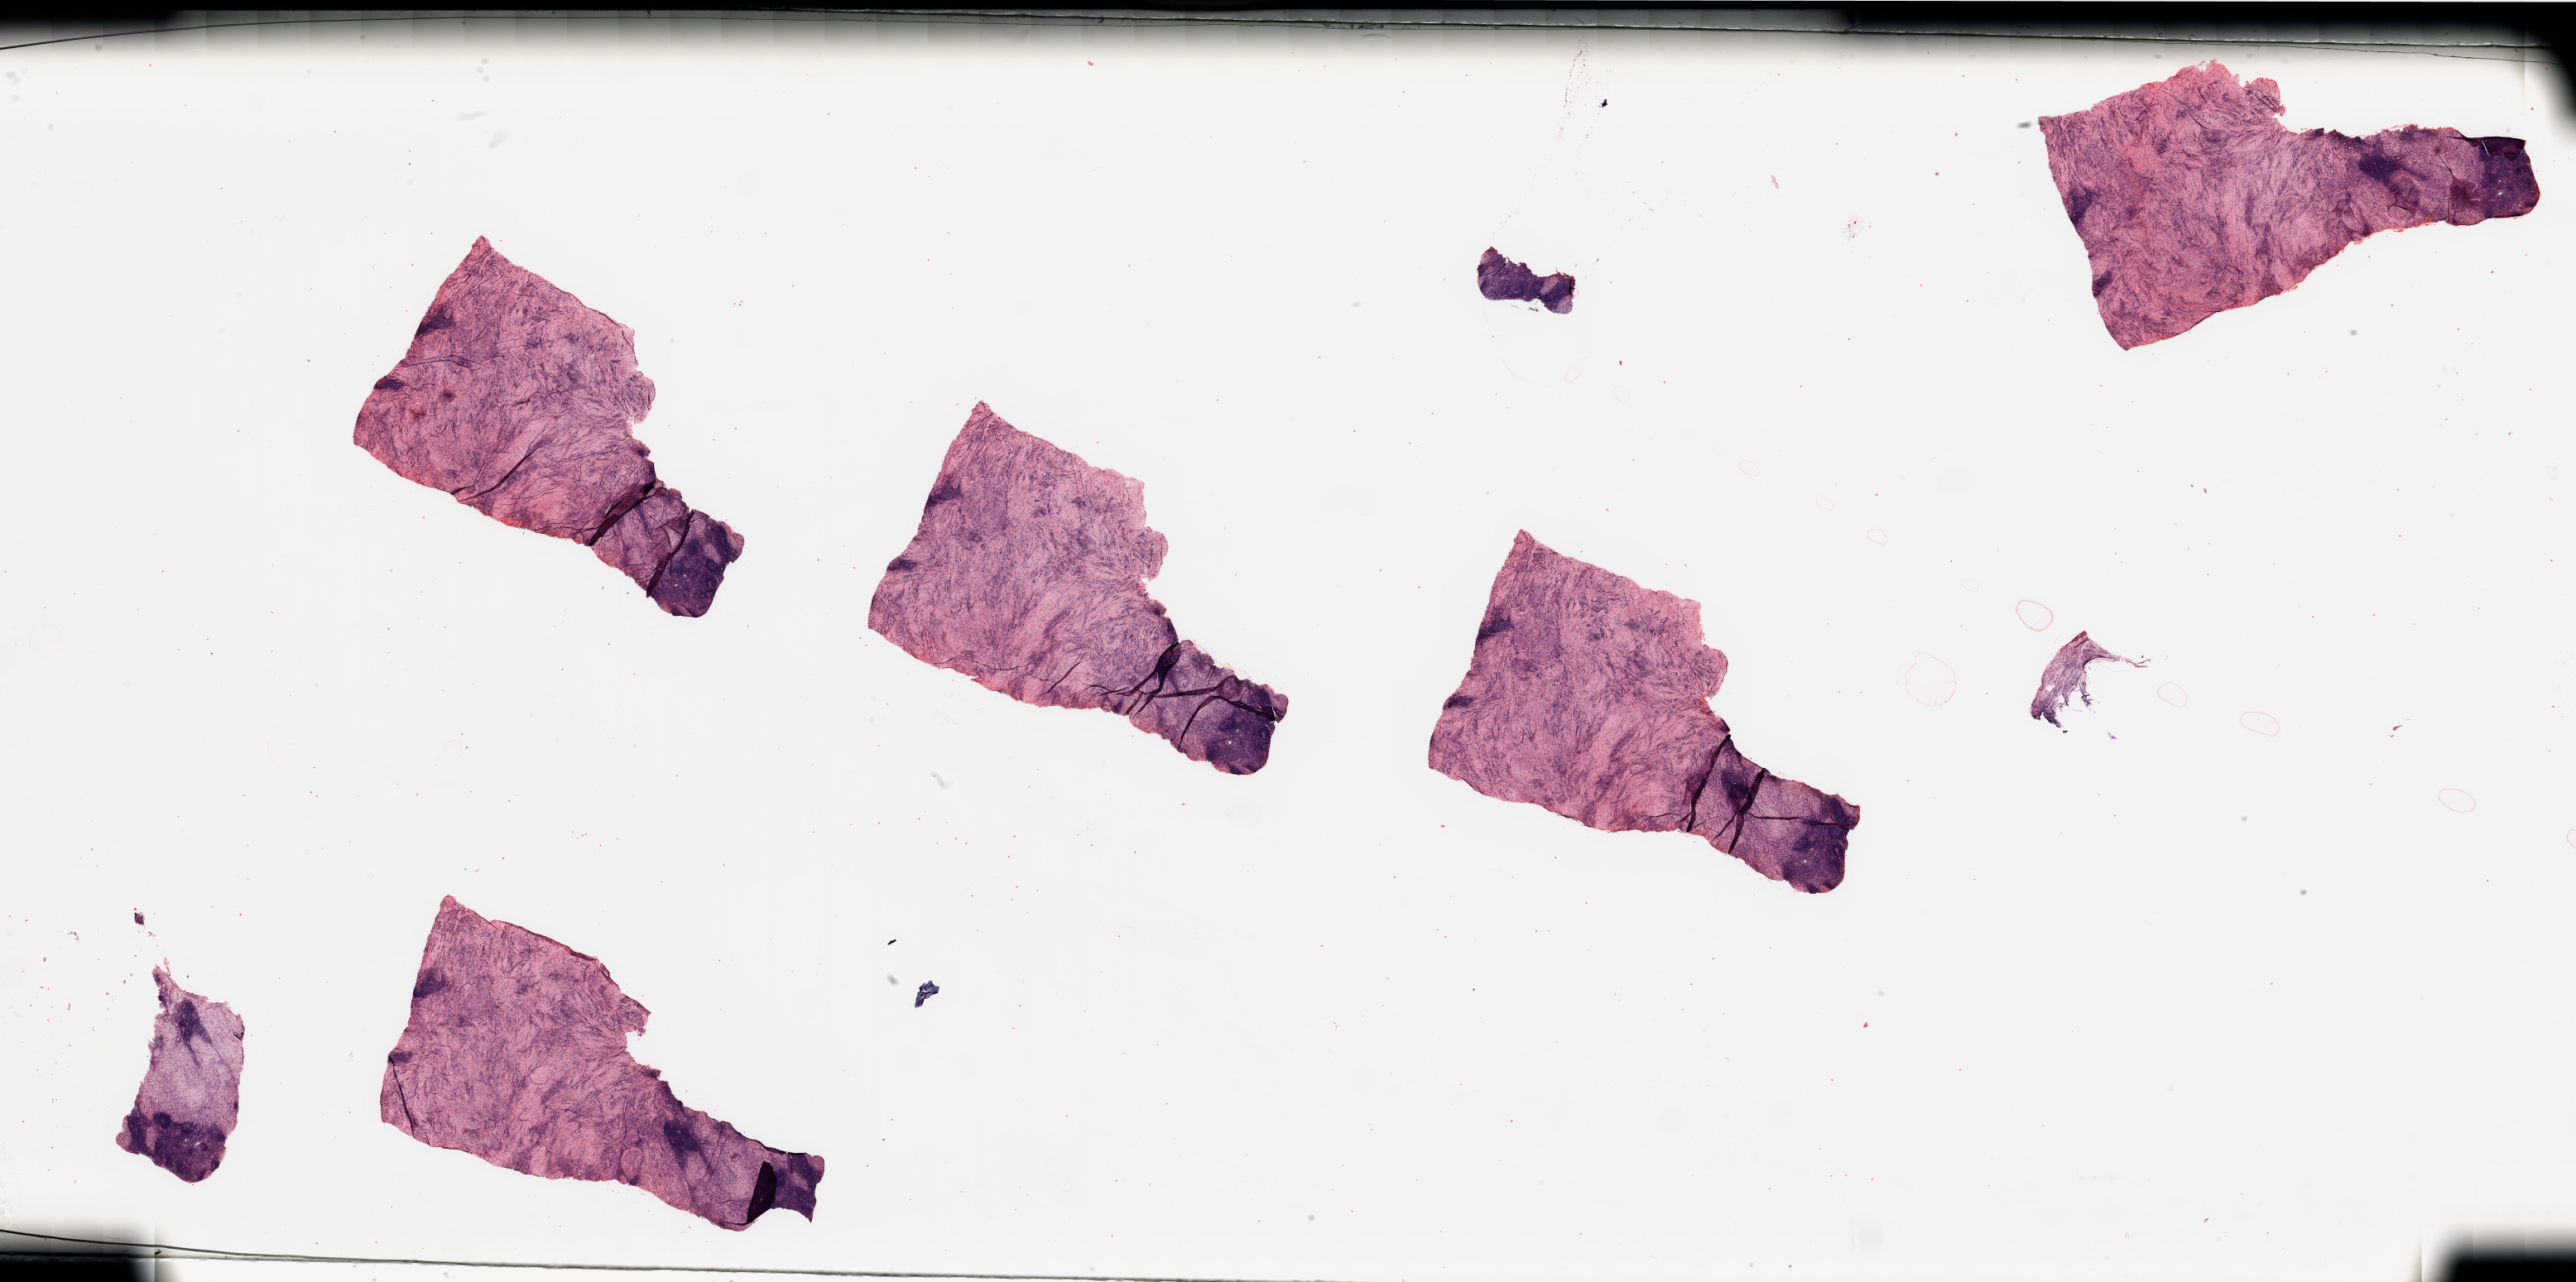
Whole-slide histology image, Hematoxylin and eosin (H&E) stained — whole scanned area (about 49.2 x 24.5 mm, slide scanned at 20x) shown as a low-resolution overview, tumour tissue sample, sampled site: lymph node. Female, 58 y/o.
This section: metastatic tumour tissue. Patient diagnosis: Malignant melanoma, NOS.